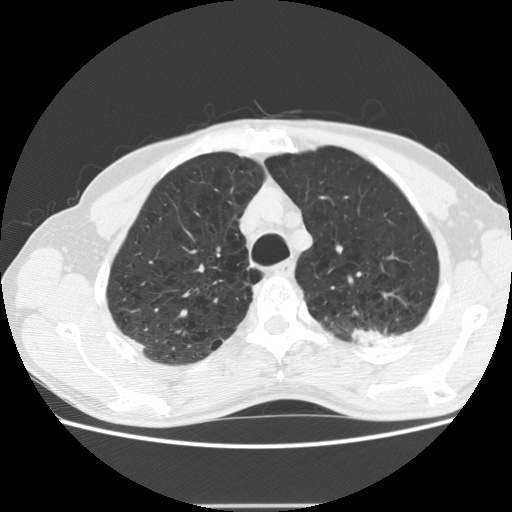
Low-dose screening chest CT, one axial slice; position 154 of 191 along the scan axis; reconstruction kernel STANDARD; lung window (W 1500 / L -600 HU); 512 × 512 image matrix, field of view 352 × 352 mm.
Structures marked on this image (manually delineated by an expert):
- lesion 1 (tumor, upper lobe of left lung): bounding box <352,329,387,343> (left, top, right, bottom; pixels)